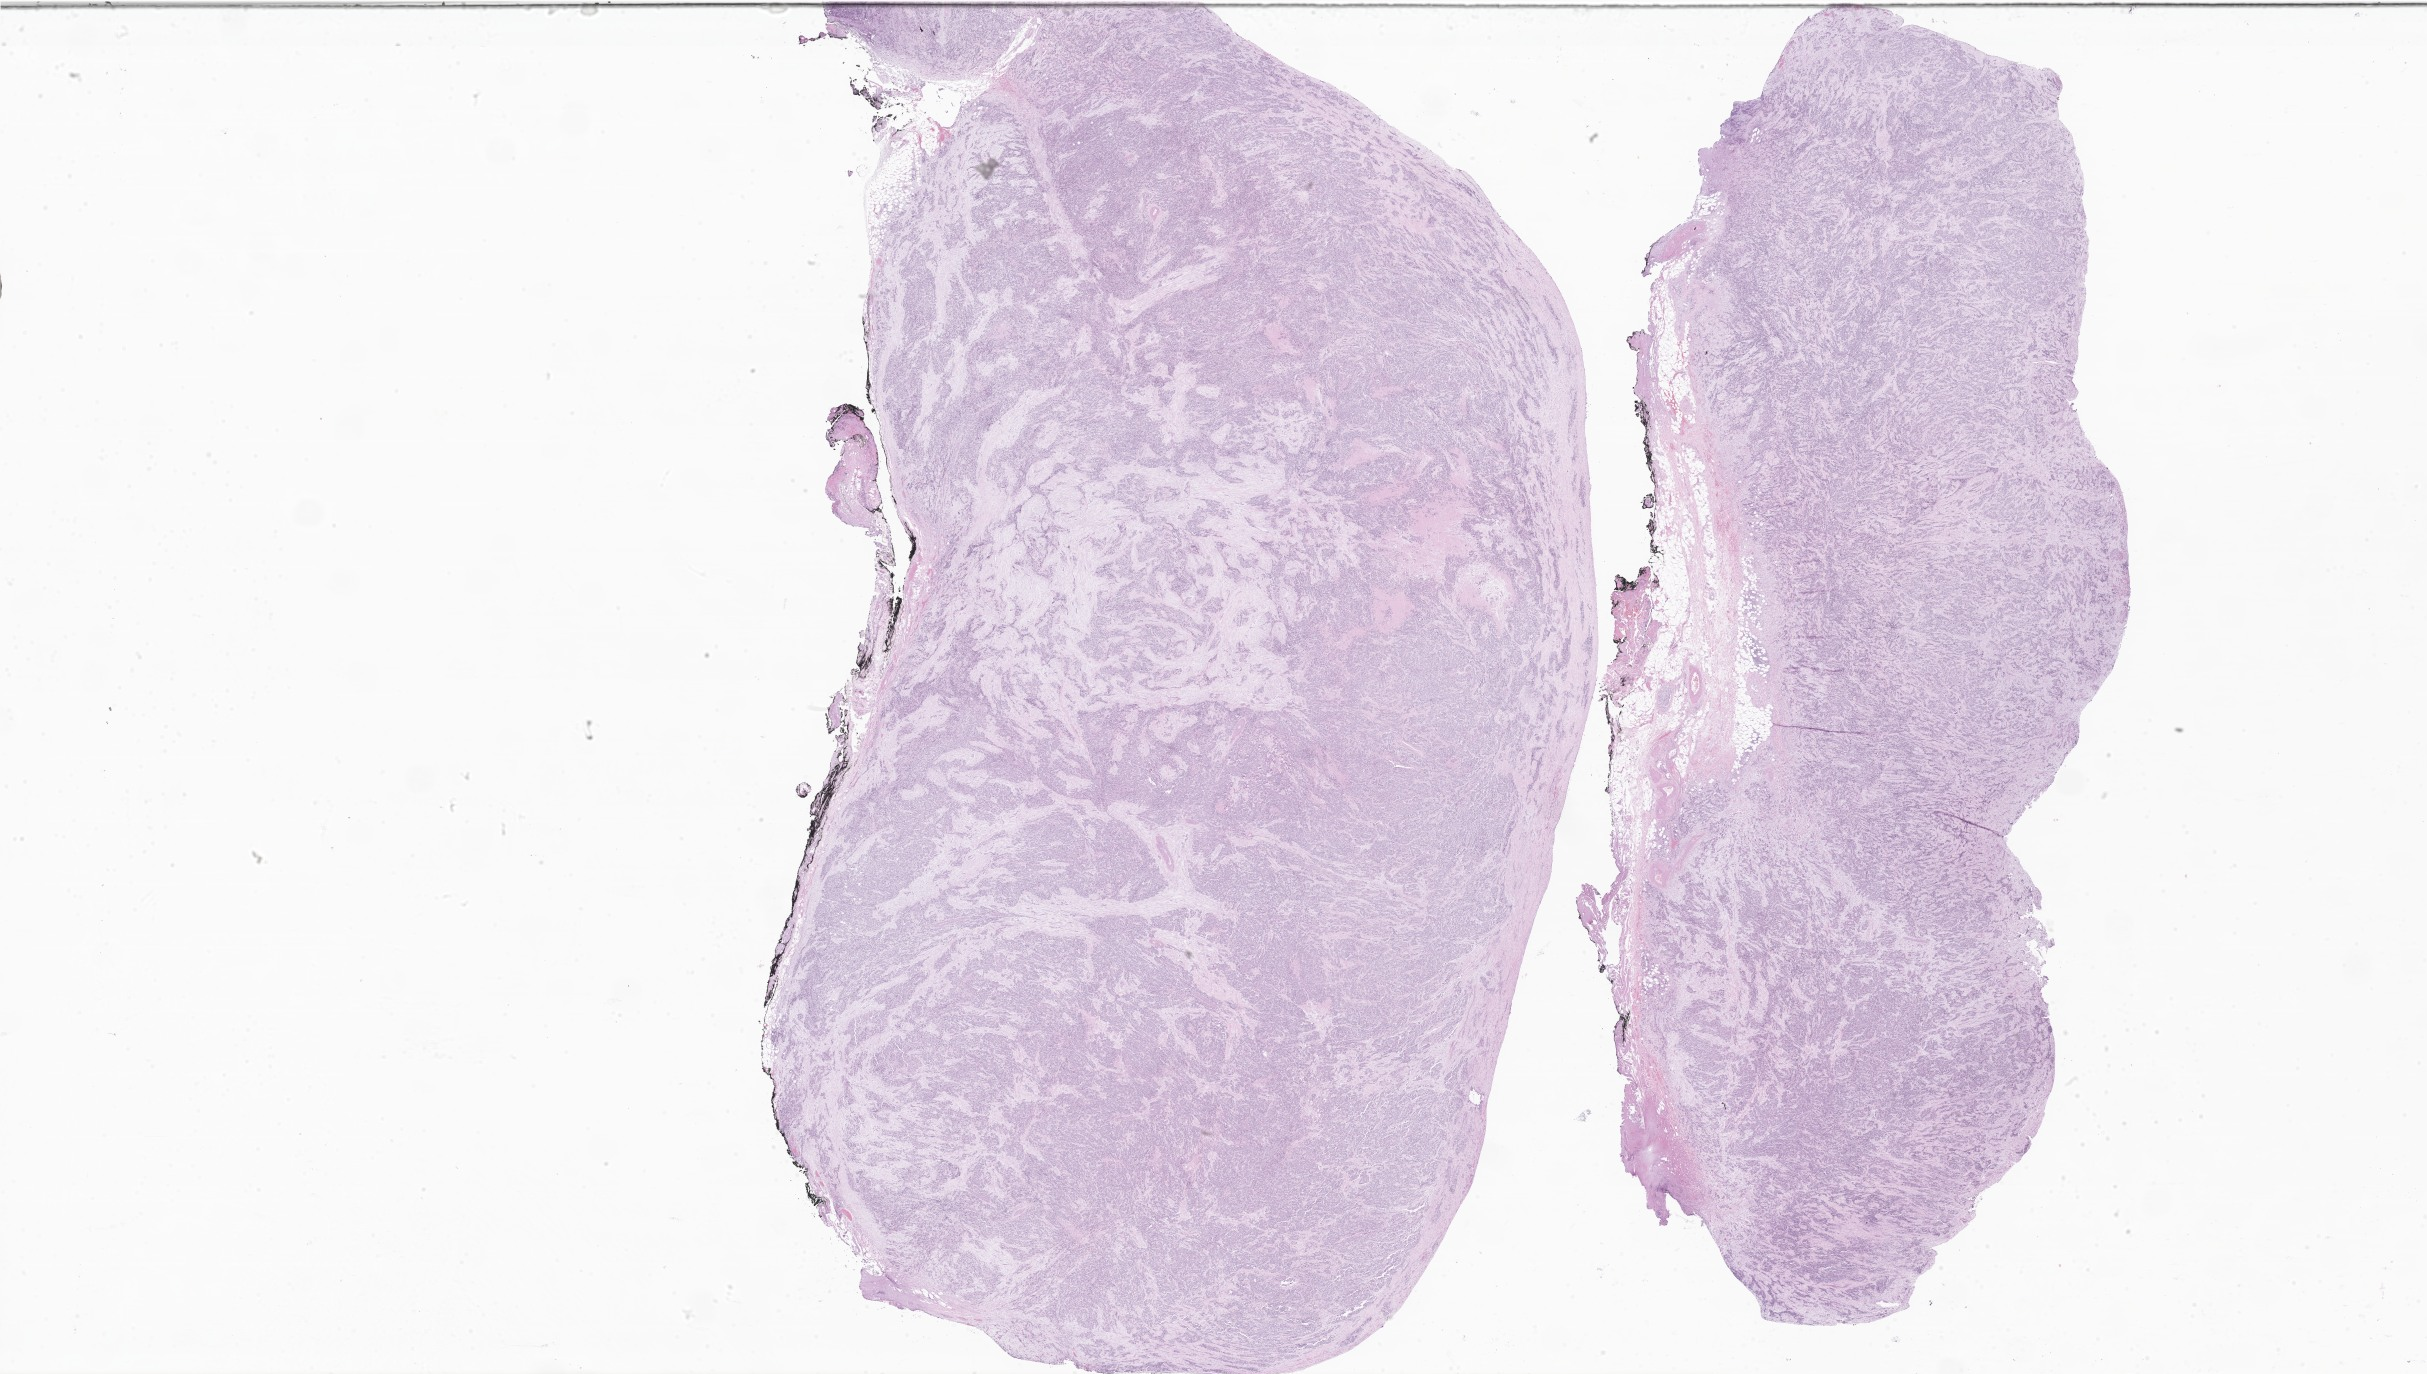
Whole-slide image, haematoxylin and eosin stain of tumor tissue from the abdomen, shown as a low-resolution overview of the whole scanned area (about 40.9 x 23.2 mm); formalin-fixed, paraffin-embedded (FFPE) tissue. Patient male; age 177 months (14 years 9 months).
• recorded diagnosis: Desmoplastic small round cell tumor